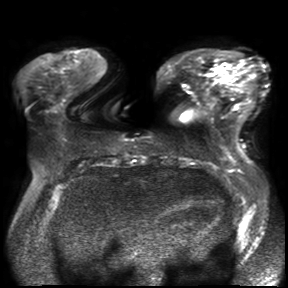
Breast MRI, one axial slice. Position 8 of 30 along the scan axis. Diffusion-weighted series; image 2 of 4 stored at this slice position (different b-values; order by instance number). 3 T. 4 mm slice thickness. 288 × 288 image matrix, field of view 360 × 360 mm. Female patient.
Outlined on this slice (expert manual segmentation):
- tumour on diffusion-weighted imaging: bounding box (x1, y1, x2, y2) in pixels: (221, 67, 235, 74)